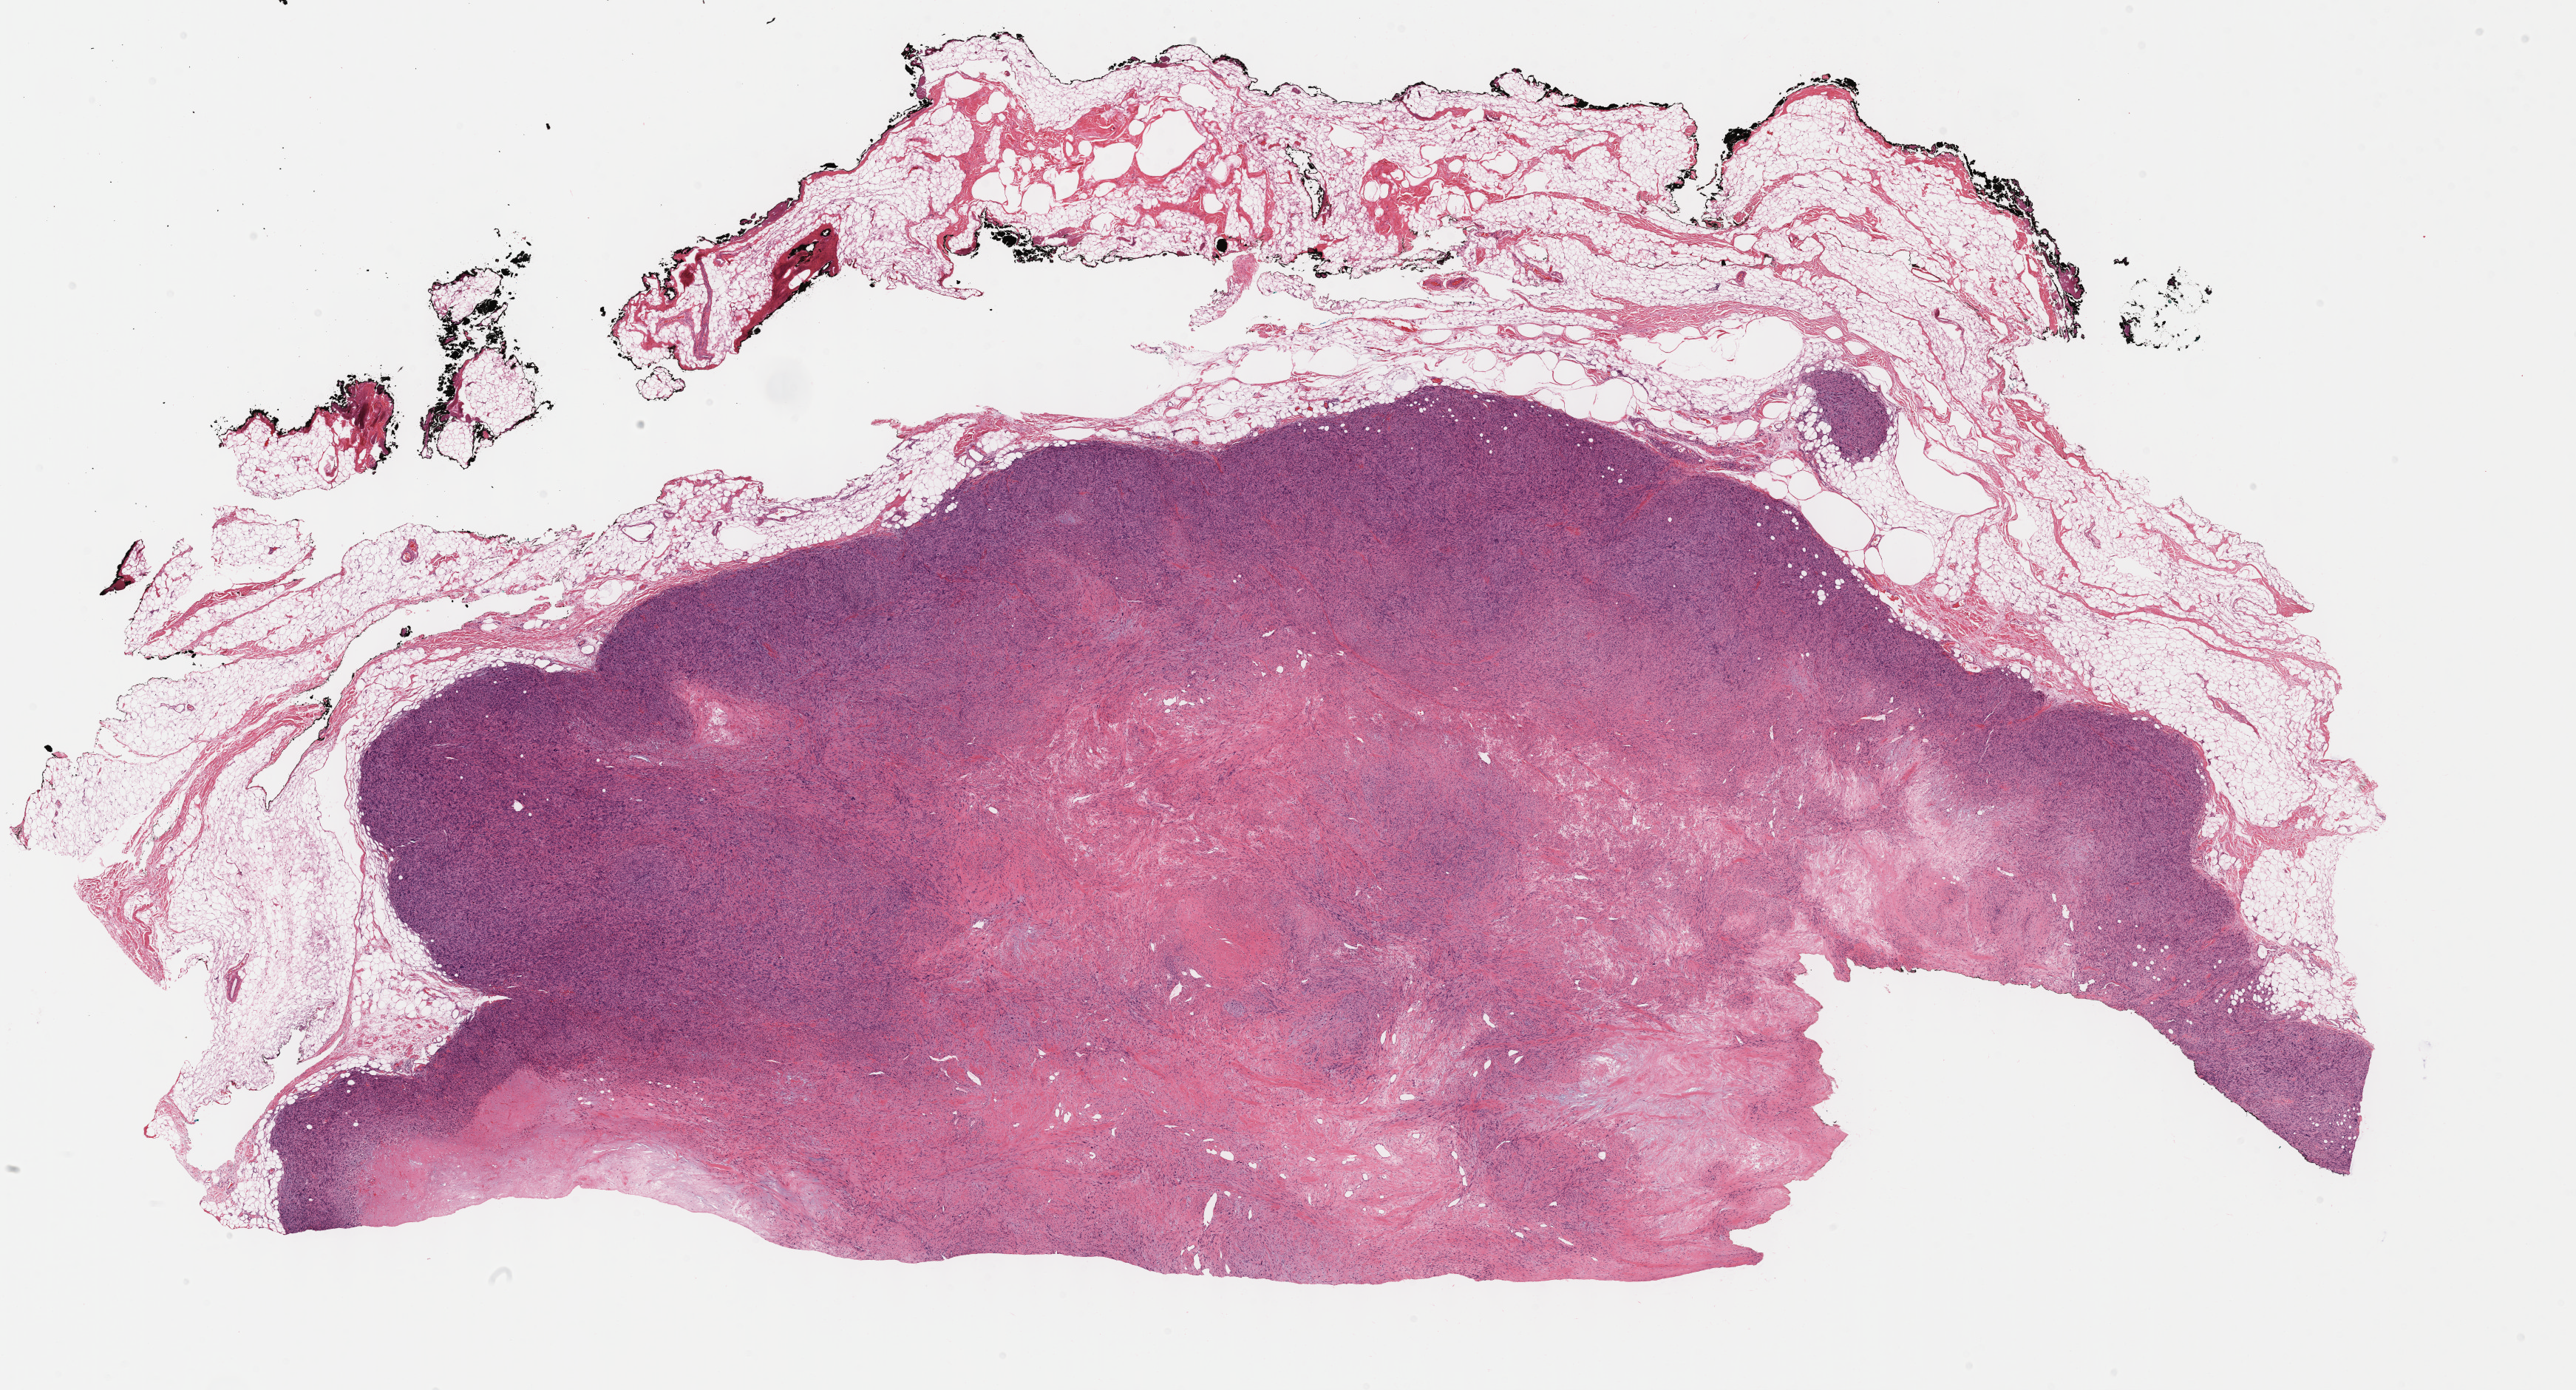
Digitized H&E tissue section (whole slide), shown as a low-resolution overview of the whole scanned area (about 28.2 x 15.2 mm, slide scanned at 40x). Formalin-fixed paraffin-embedded (FFPE) diagnostic section. Primary tumour sample from the connective, subcutaneous and other soft tissues. Female patient; age at initial diagnosis 52 years.
Histologic diagnosis: Leiomyosarcoma, NOS.